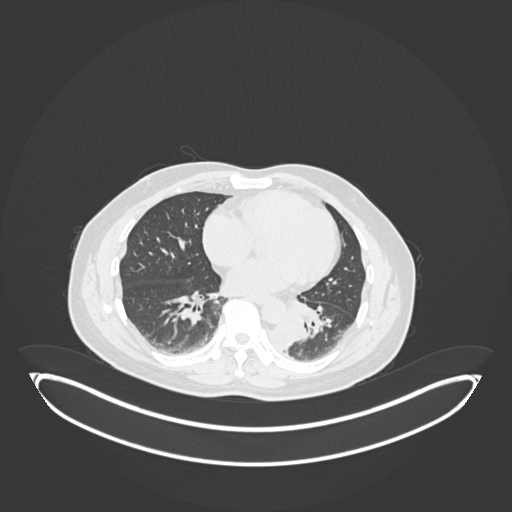
Chest CT, one axial slice; position 73 of 258 along the scan axis; reconstruction kernel B30f; lung window (W 1500 / L -600 HU); 1 mm slice thickness; 512 × 512 image matrix, field of view 500 × 500 mm. Male patient, age 54 years. Case-level facts recorded for this patient, not image findings: clinical TNM (as recorded): T3 N0 M0.
Structures marked on this image (bounding box drawn by a radiologist):
- lung tumour (recorded histology: squamous cell carcinoma): bounding box <262,313,308,352> (left, top, right, bottom; pixels)